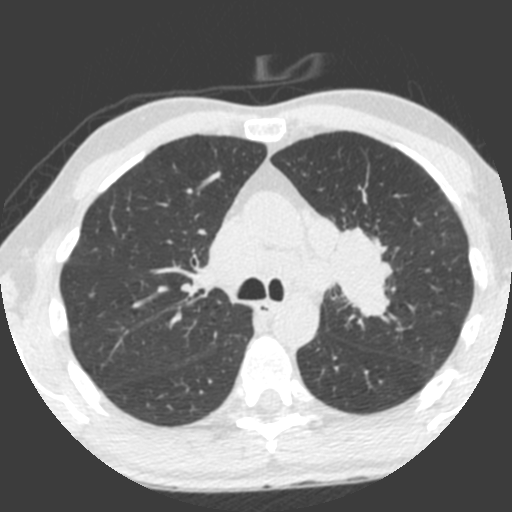
Low-dose screening chest CT, axial slice. Third annual screen. Lung window (W 1500 / L -600 HU). 2 mm slice thickness. 512 × 512 image matrix. Male, age 55 years at enrolment.
• Expert reader's lesion annotation, bounding box <309,227,393,323> (left, top, right, bottom; pixels).
• Screening reader's record for this exam (one nodule recorded; not confirmed to be the boxed lesion): non-calcified nodule or mass ≥4 mm, left upper lobe, 49 × 29 mm, spiculated (stellate) margins, soft tissue attenuation, pre-existing on the prior screen: yes; interval growth: yes.